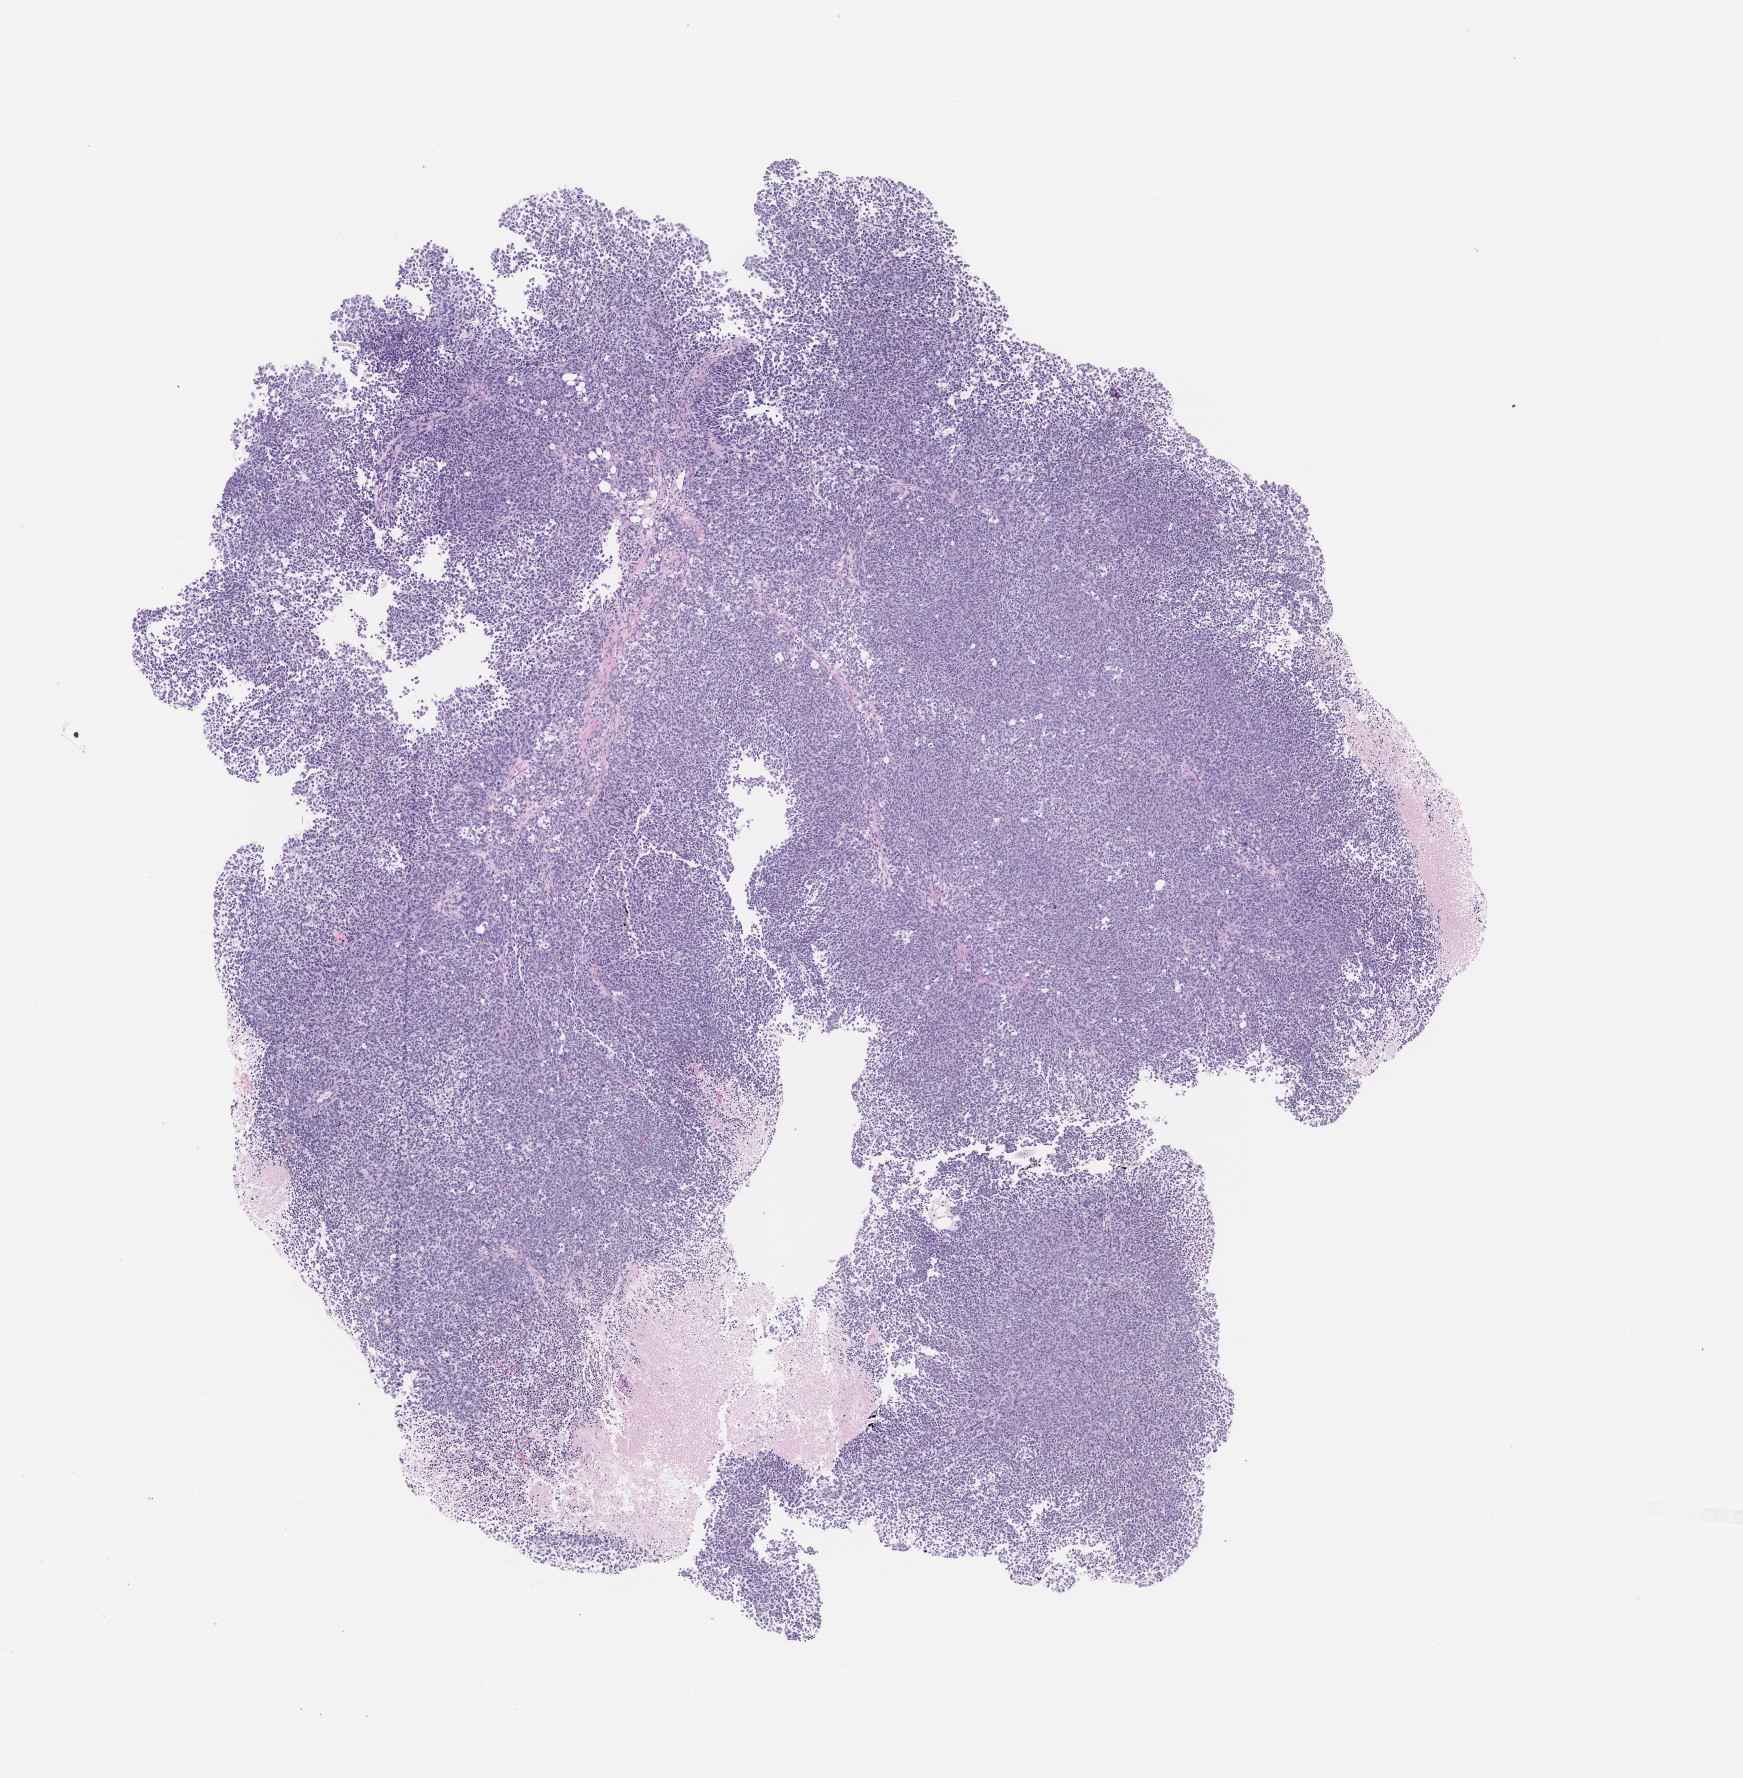
Hematoxylin and eosin (H&E) whole-slide image of a patient-derived xenograft (PDX) tumor grown in a mouse, passage 0 — whole scanned area (about 7.0 x 7.2 mm) shown as a low-resolution overview, formalin-fixed, paraffin-embedded (FFPE) tissue, originating tumor site category: musculoskeletal.
Originating patient diagnosis: Ewing Sarcoma|Primitive Neuroectodermal Tumor.